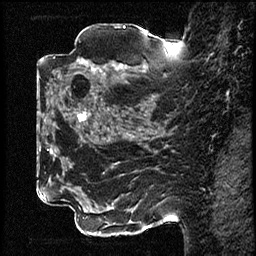
Breast MRI (dynamic contrast-enhanced), one sagittal slice. Slice 33 of 78 in the series (ordered by position). Dynamic contrast-enhanced study with each time point stored as its own series, time point 2 of 3 at this slice position (early post-contrast, ordered by acquisition time). 1.5 T. TE 4.2 ms, TR 17.6 ms. 256 × 256 image matrix. Patient: female, 42 years. From the clinical record (not read from this slice): setting: breast cancer imaged before/during neoadjuvant chemotherapy; receptor status: HER2-positive.
Outlined on this slice (semi-automatically segmented with operator editing):
- analysis volume of interest (the breast-tissue region the enhancement analysis was run in; not a lesion): bounding box <50,48,131,129> (left, top, right, bottom; pixels)
- tumour enhancement mask (voxels above the 100 % enhancement threshold inside the analysis volume of interest): <77,67,99,121>